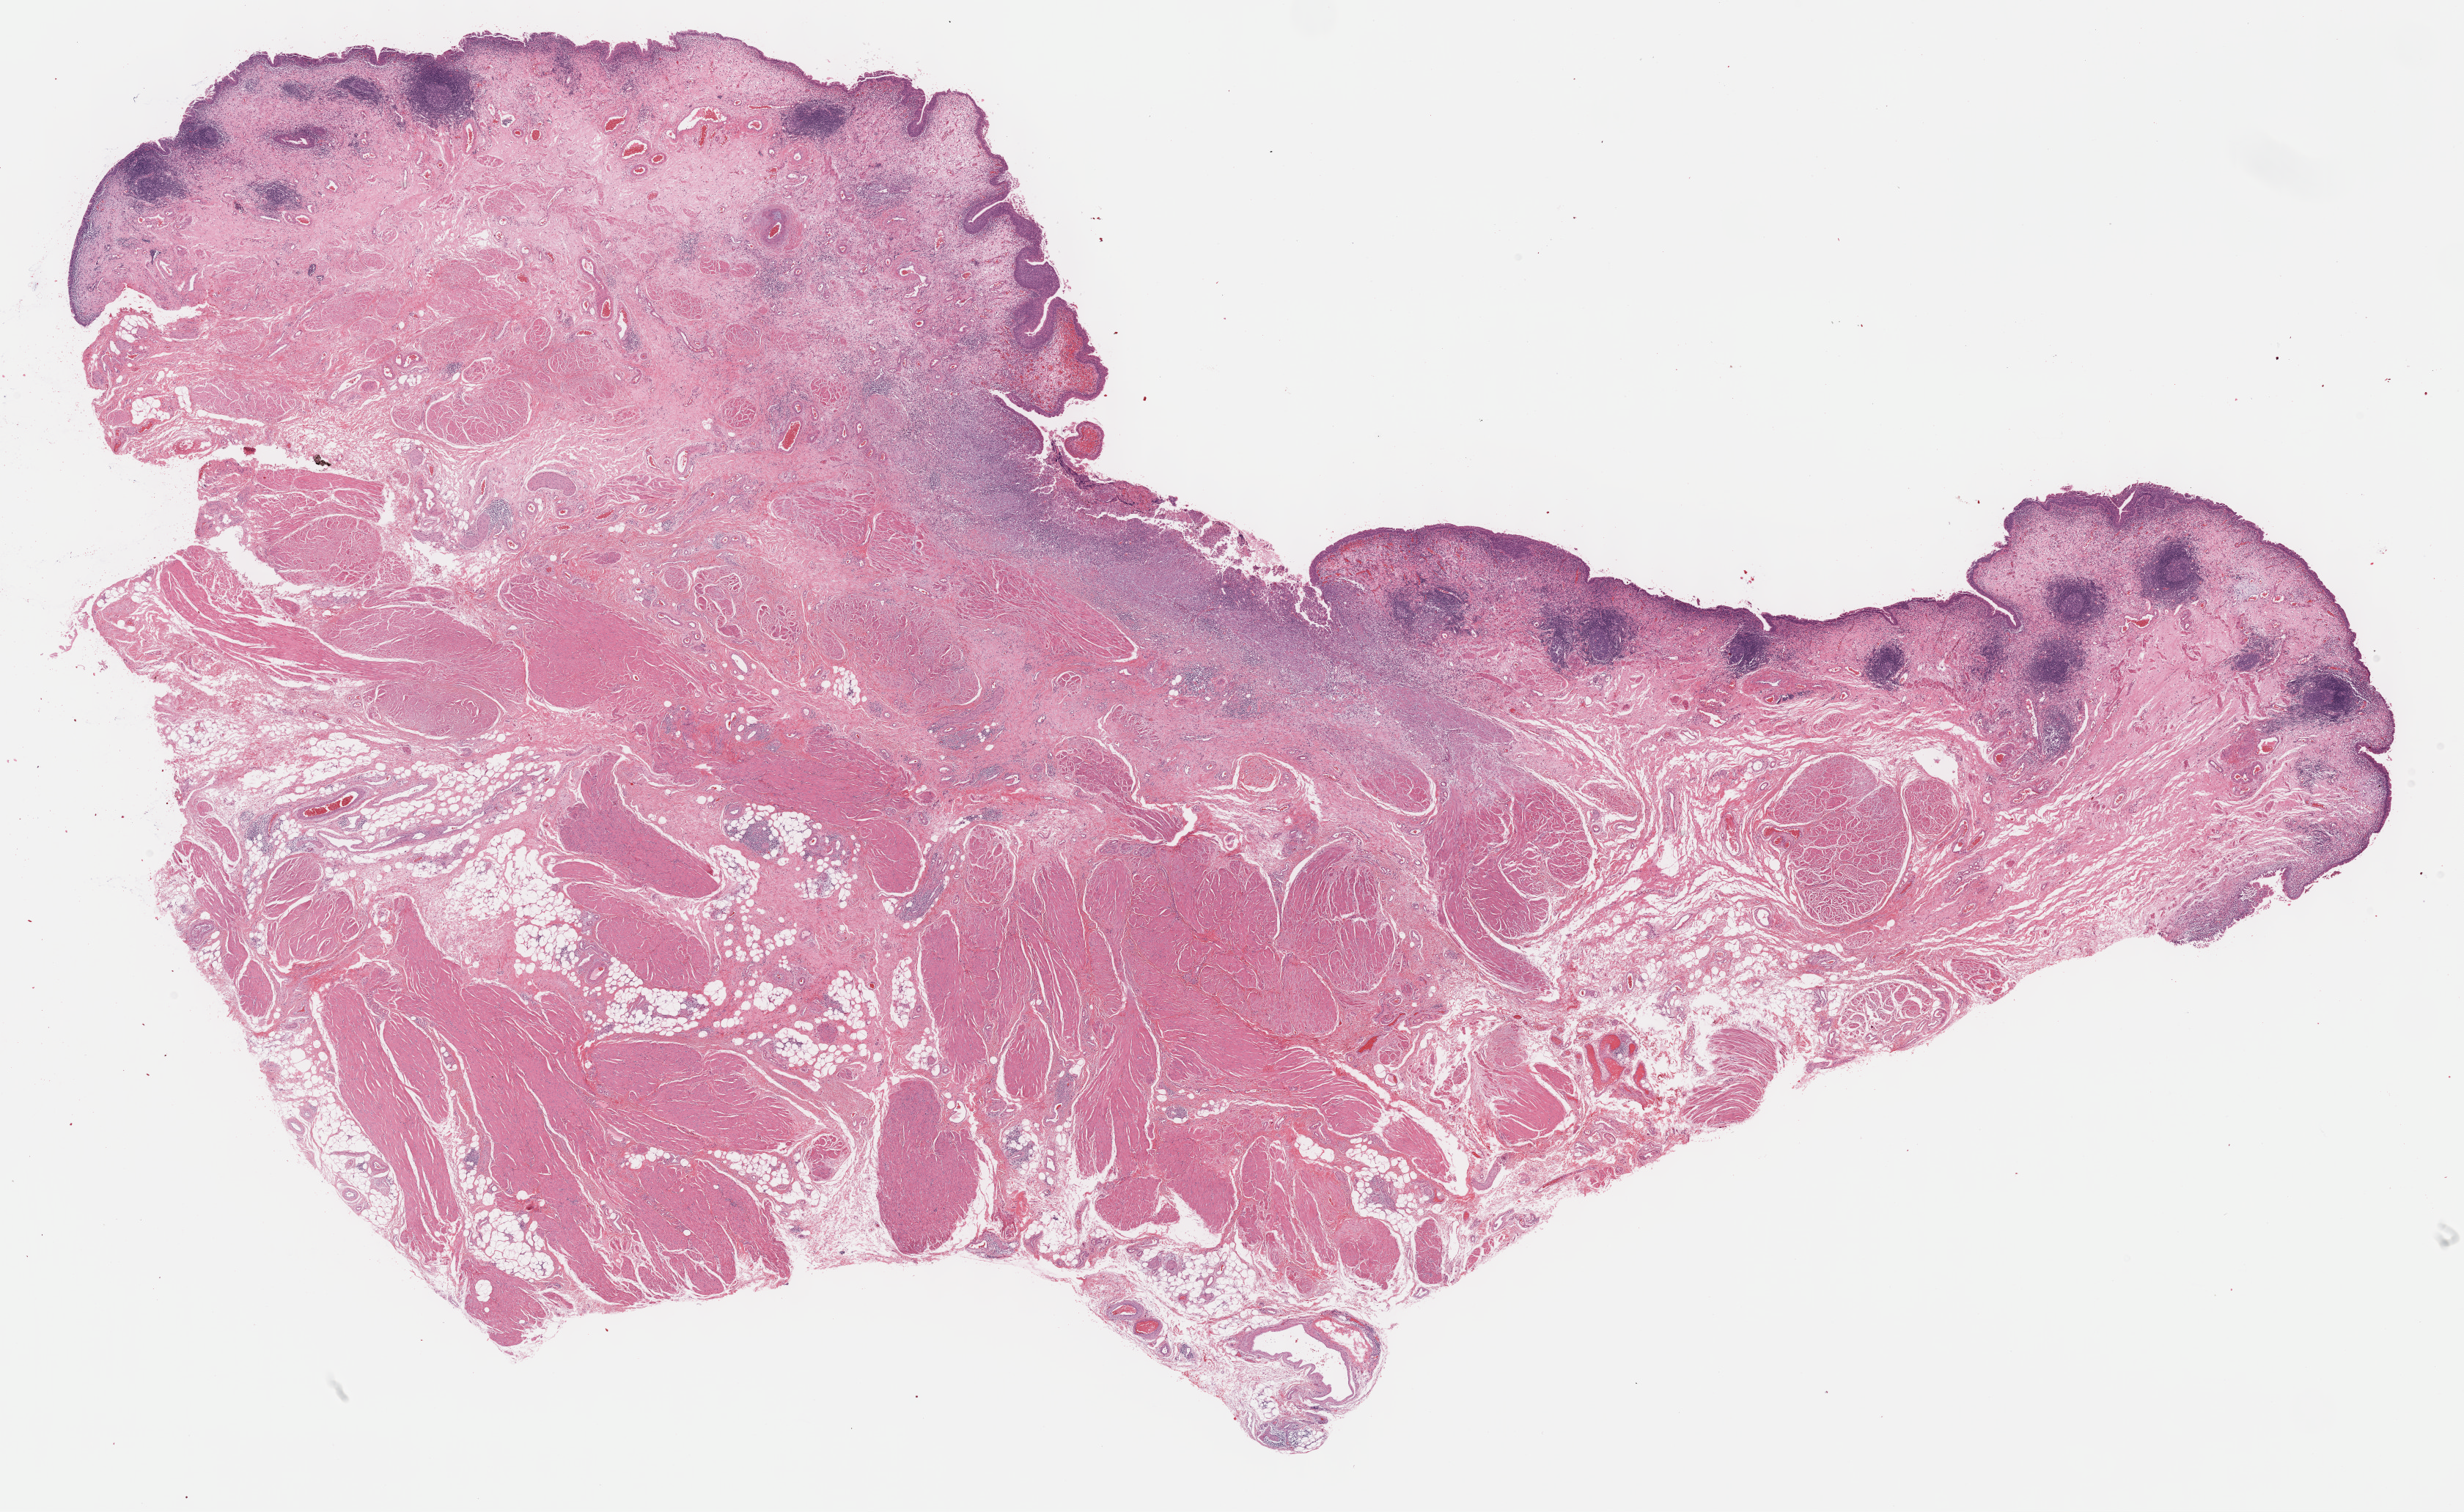
Digitized Hematoxylin and eosin (H&E) stained tissue section (whole slide), whole scanned area (about 27.2 x 16.7 mm, from a 40x scan) shown as a low-resolution overview. Formalin-fixed paraffin-embedded (FFPE) diagnostic section. Sample: primary tumour, bladder. Female, age 59 years at initial diagnosis. Histologic grade: high grade.
Diagnosis: Papillary transitional cell carcinoma. Lymph nodes positive (case pathology): 0 of 67 examined. AJCC pathologic stage: II (6th edition).